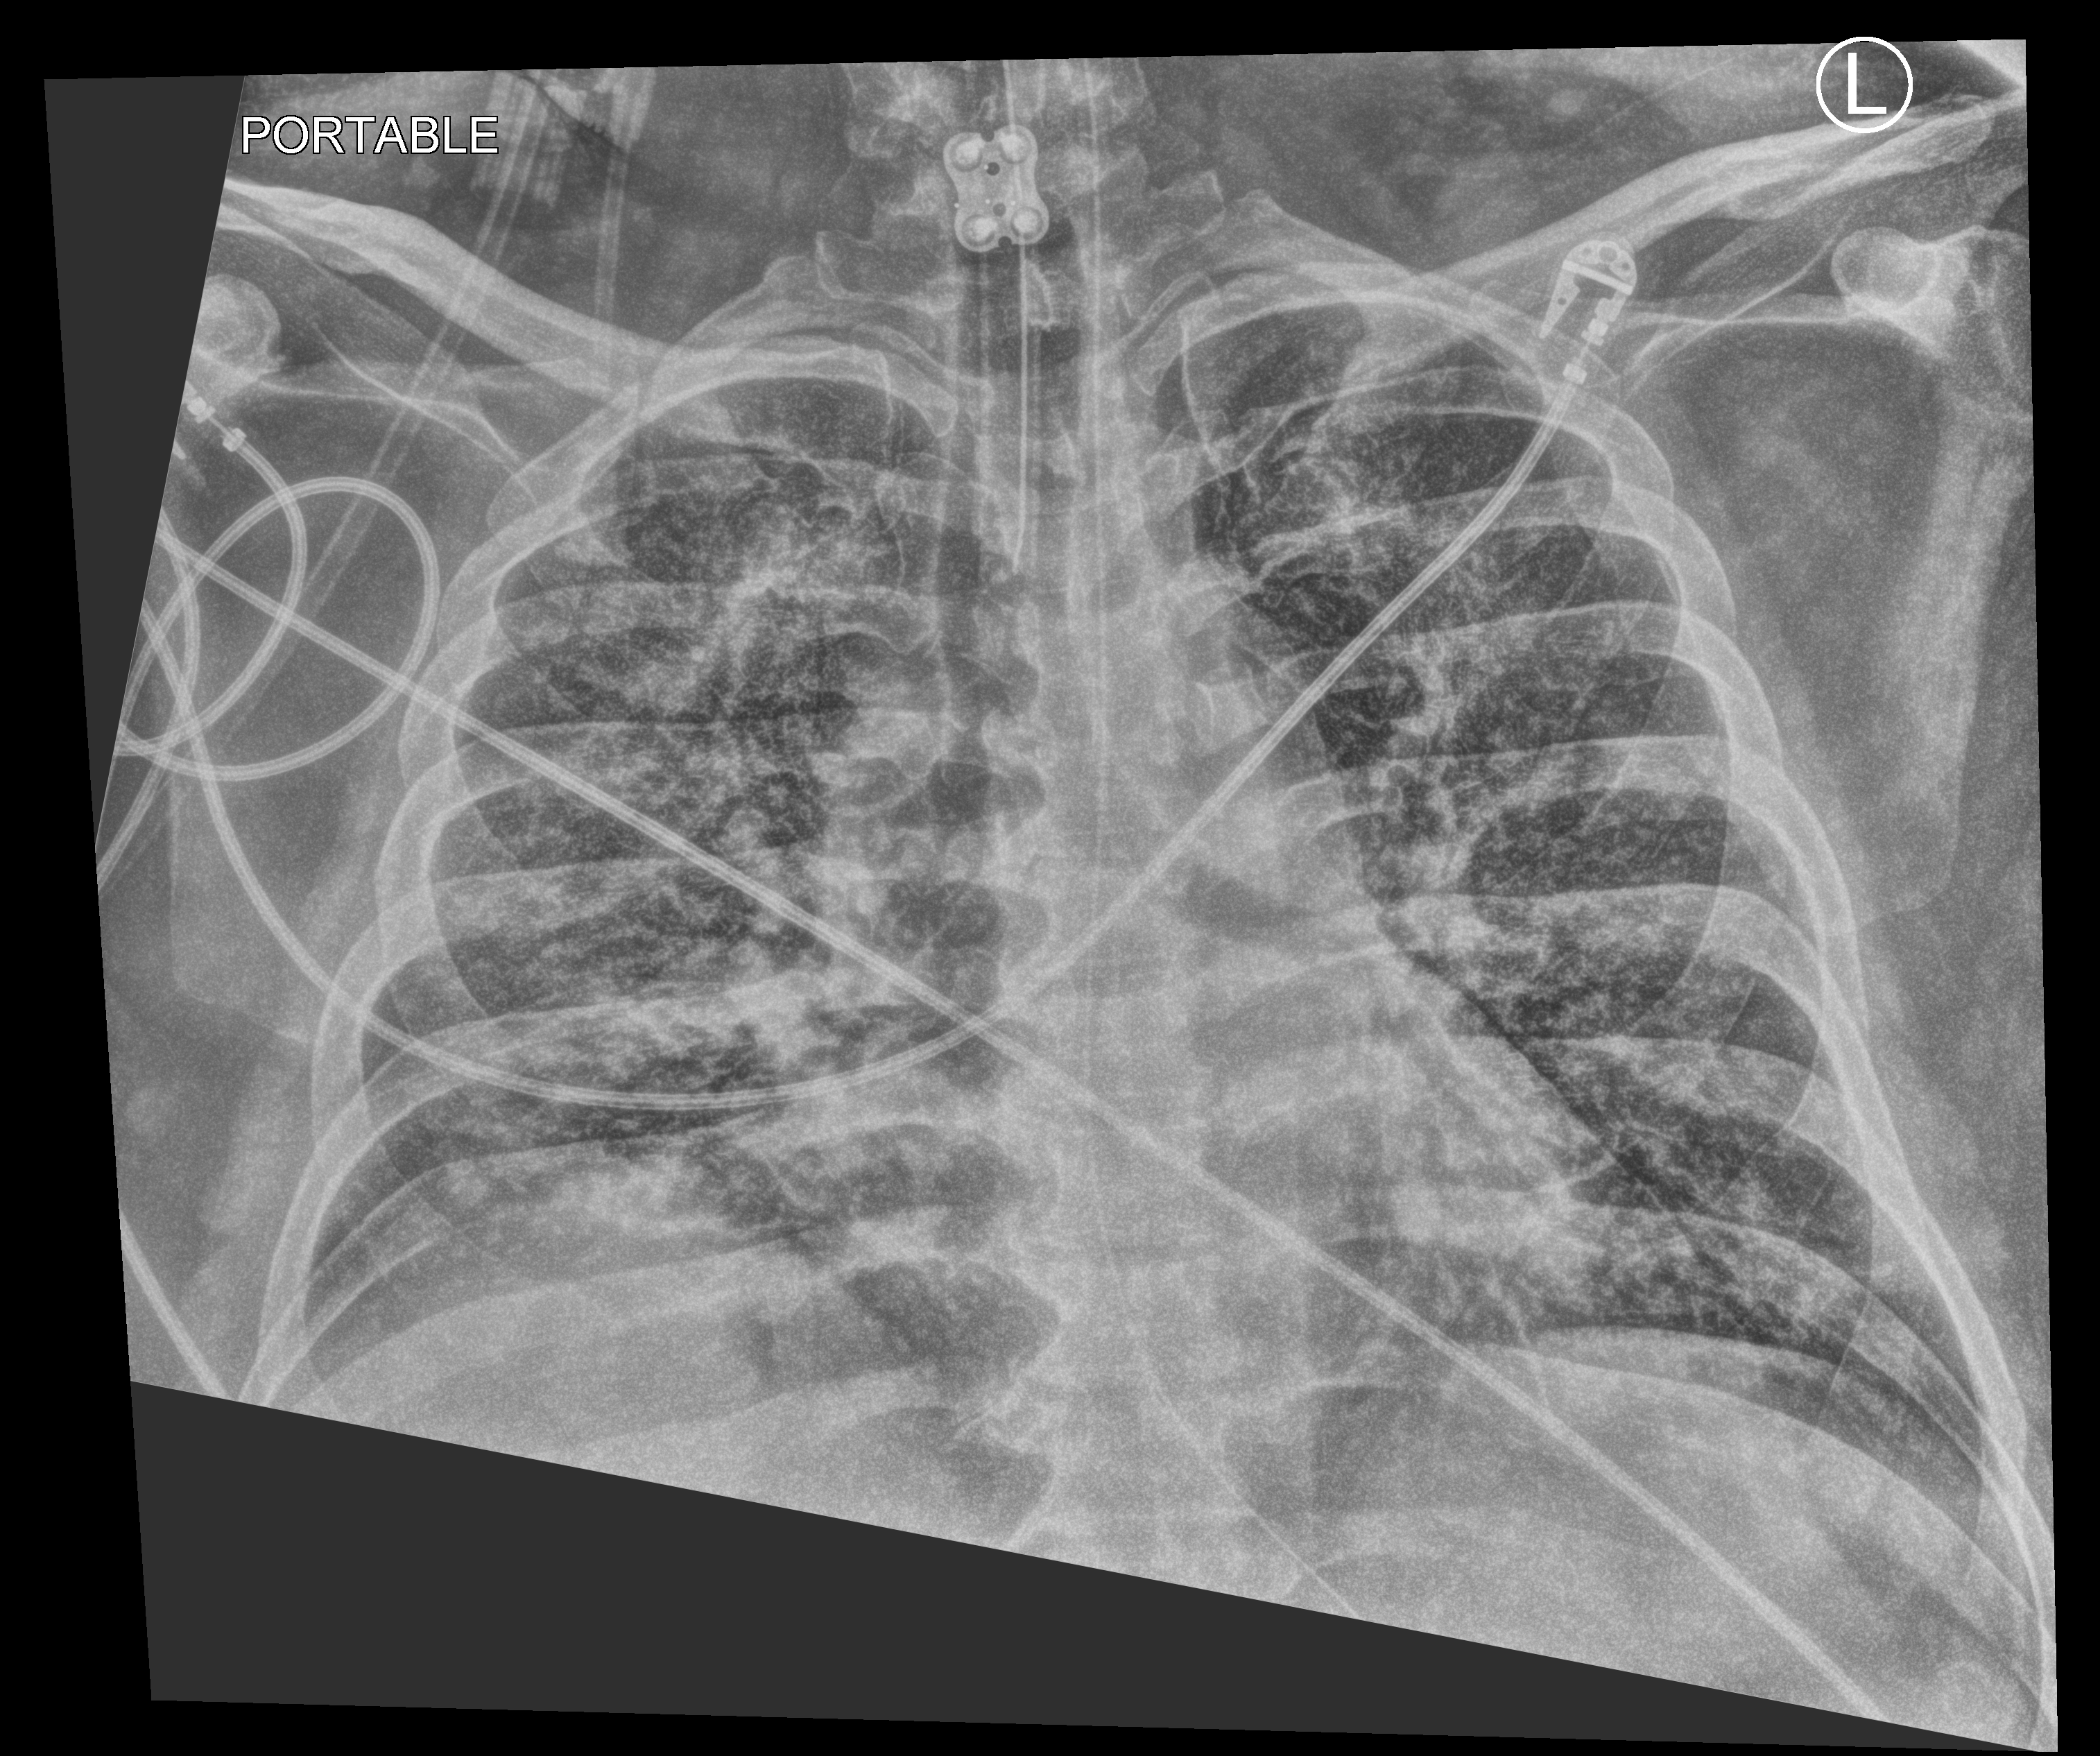
Bedside chest radiograph (computed radiography), anteroposterior (AP) projection. Male patient hospitalised with COVID-19, age 18–59 years.
From the hospital-stay record, not from the radiograph (when in the stay this image was taken is not recorded): admitted to intensive care during this hospital stay: yes; chronic kidney disease (admission record): no; mechanically ventilated during this hospital stay: yes.